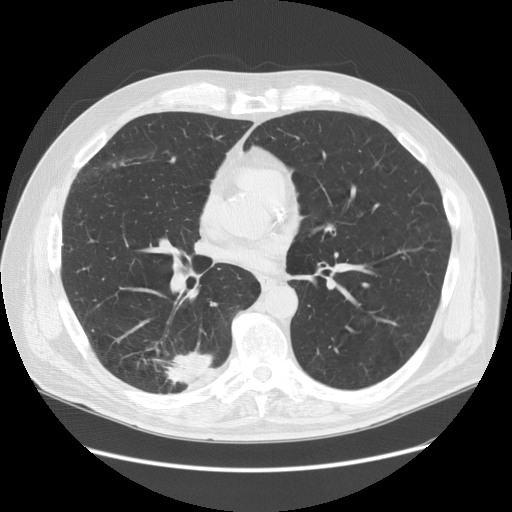
Axial slice from a low-dose chest CT screening exam; baseline annual screen; lung window (W 1500 / L -600 HU); slice 78 of 149 in the series; 512 × 512 image matrix. Male participant, aged 68 years at enrolment. Former smoker at enrolment.
- Expert-annotated lung lesion, box from (x=126, y=338) to (x=226, y=411) px.
- Screening reader's record for this exam (one nodule recorded; not confirmed to be the boxed lesion): non-calcified nodule or mass ≥4 mm, right lower lobe, 37 × 20 mm, spiculated (stellate) margins, soft tissue attenuation.
- Official screen result: positive, change unspecified: nodule(s) >= 4 mm or enlarging nodule(s), mass(es), or other non-specific abnormalities suspicious for lung cancer.
- Lung cancer was diagnosed 24 days after this screen: adenosquamous carcinoma, right lower lobe, poorly differentiated (G3), stage IIIA (AJCC 6th edition), 30 mm at pathology.